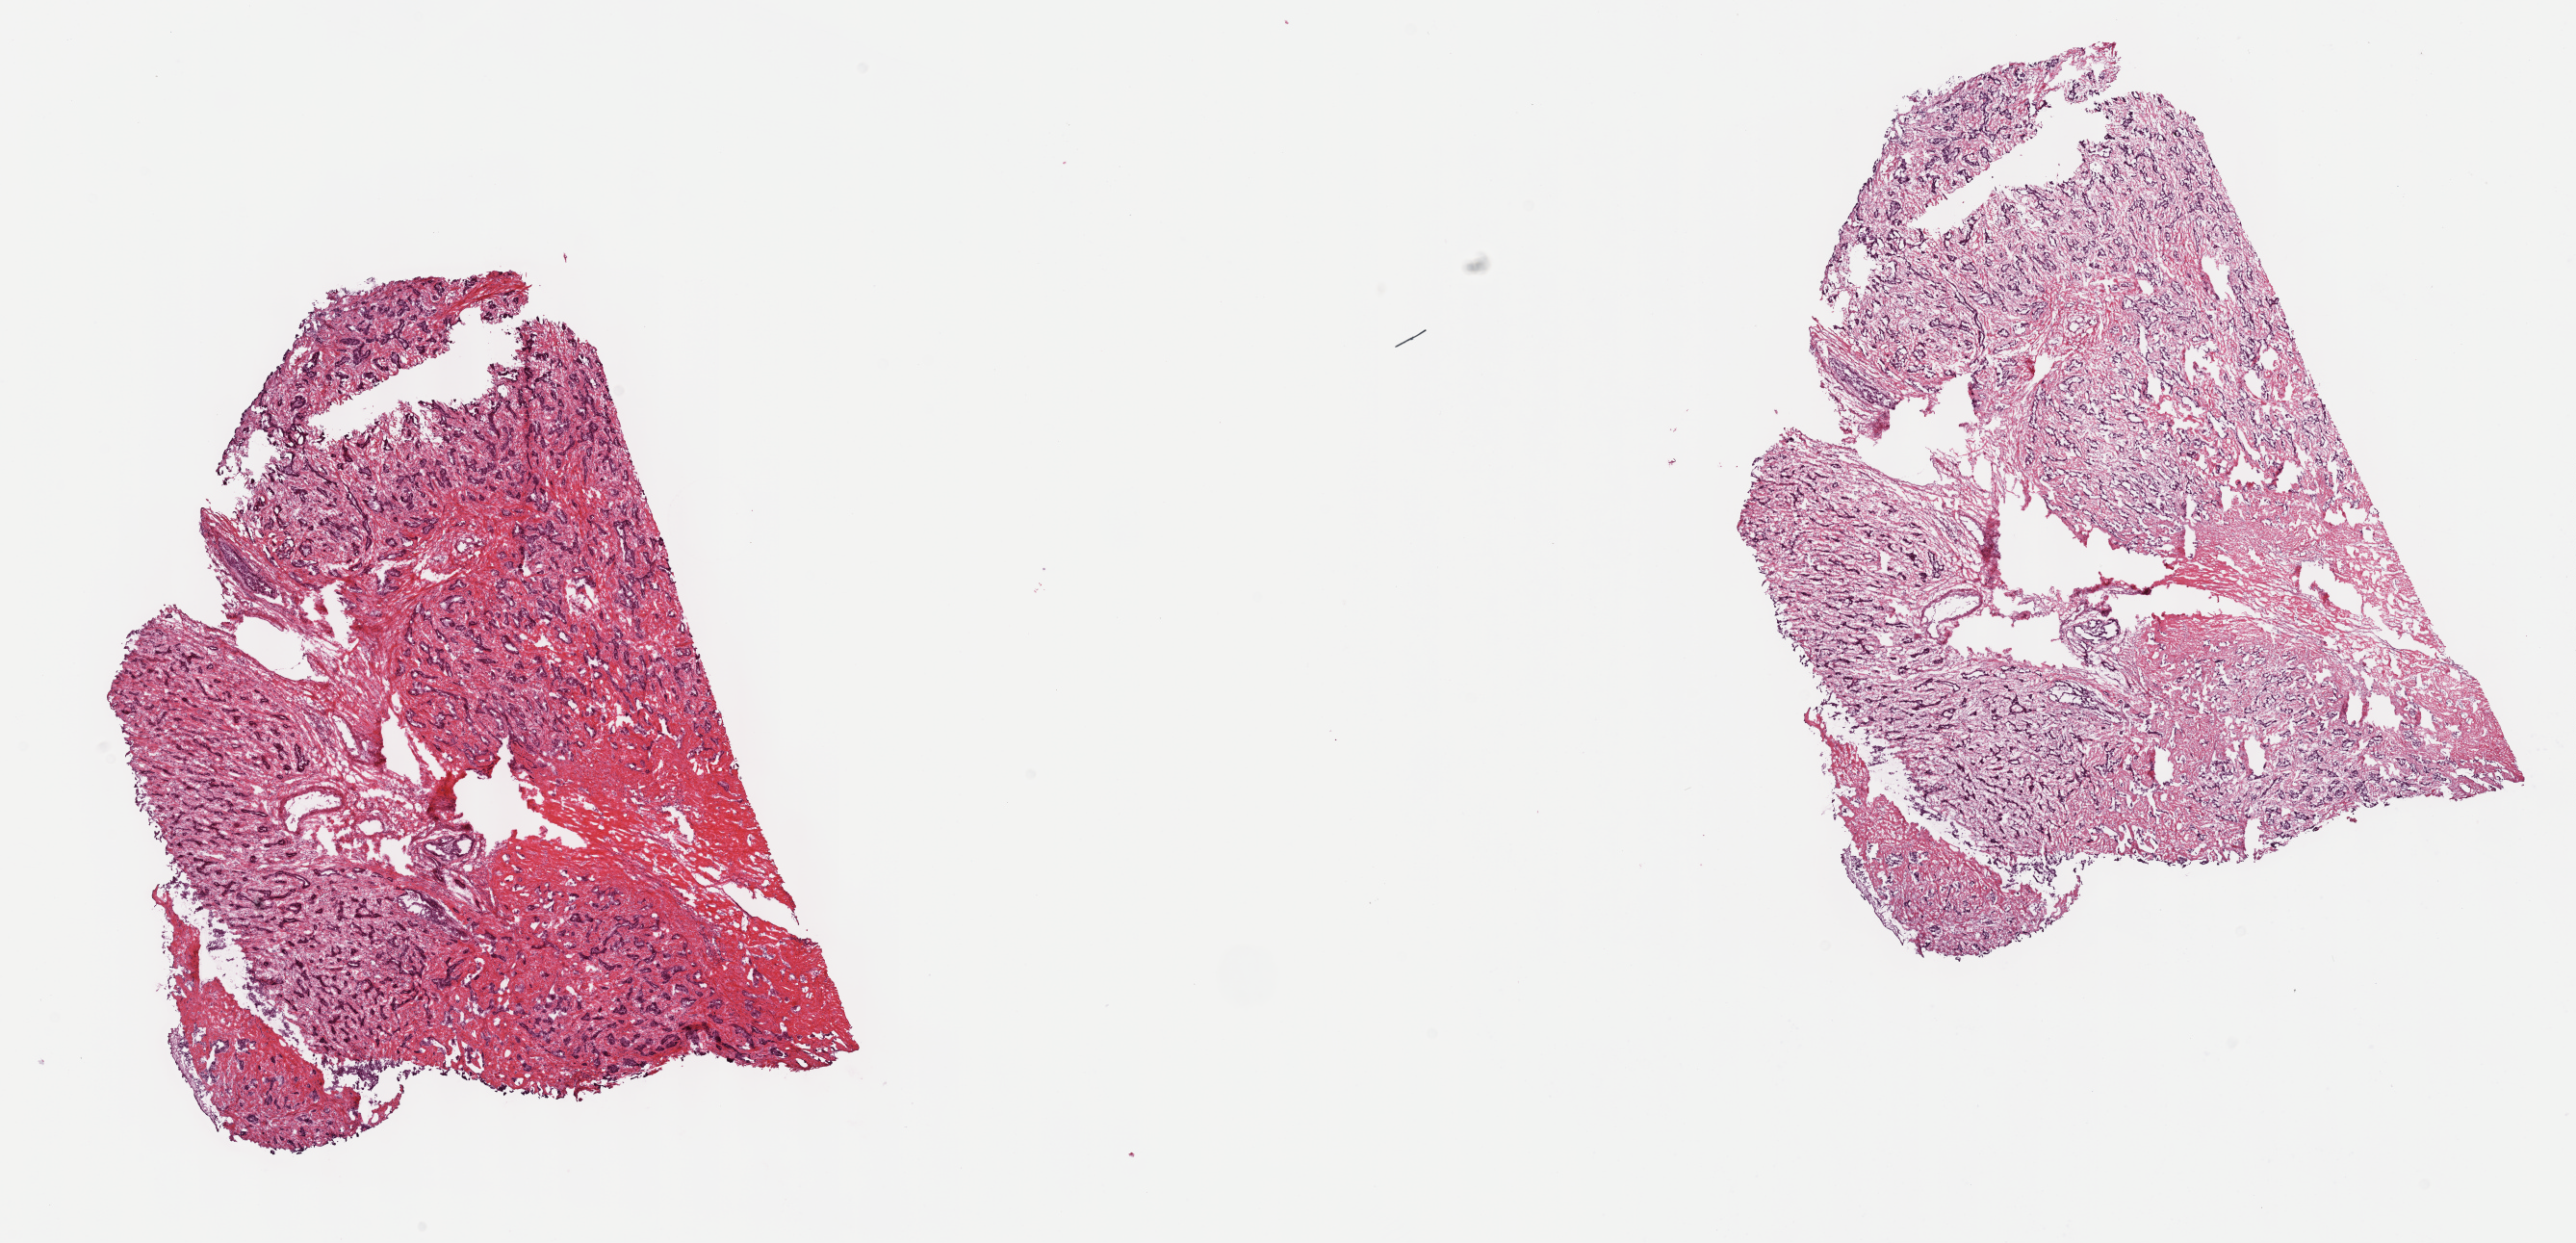
Whole-slide histology image, H&E, whole scanned area (about 21.6 x 10.4 mm) shown as a low-resolution overview, frozen section, sample: primary tumour, bile duct. Male patient; age at initial diagnosis 62 years. Histologic grade: G2 (moderately differentiated). Composition of this section per pathologist review: tumour cells 70%, tumour nuclei 70%, normal cells 0%, stromal cells 30%, necrosis 0%. Inflammatory infiltration, as recorded: lymphocyte infiltration 3%, monocyte infiltration 1%, neutrophil infiltration 4%.
AJCC pathologic stage: I (7th edition). Diagnosis: Cholangiocarcinoma (intrahepatic bile duct).